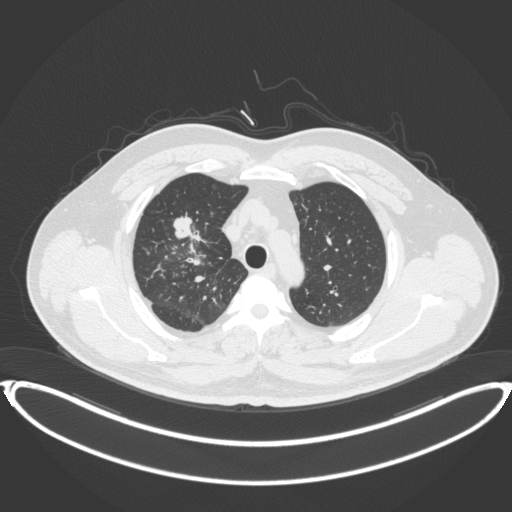
Chest CT, one axial slice; slice 301 of 399 in the series (ordered by position); reconstruction kernel B31f; lung window (W 1500 / L -600 HU); 1 mm slice thickness; 512 × 512 image matrix, field of view 445 × 445 mm. Patient: male, 53 years. From the clinical record (not read from this slice): clinical TNM (as recorded): T2a N0 M0.
Annotated regions visible in this slice (bounding box drawn by a radiologist):
- lung tumour (recorded histology: adenocarcinoma): bounding box [x1, y1, x2, y2] px = [167, 209, 205, 247]